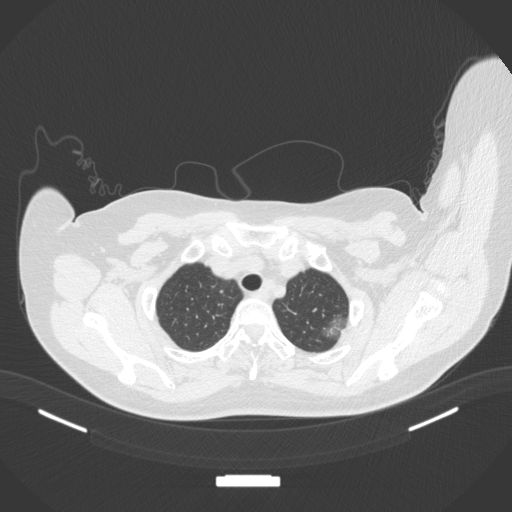
Chest CT, one axial slice; slice 321 of 386 in the series (ordered by position); reconstruction kernel B31f; 120 kVp; lung window (W 1500 / L -600 HU); 1 mm slice thickness; 512 × 512 image matrix. Patient: female, 58 years. Case-level facts recorded for this patient, not image findings: clinical TNM (as recorded): T1c N0 M0.
Outlined on this slice (rectangle marked by the reading radiologist):
- lung tumour (recorded histology: adenocarcinoma): bounding box [x1, y1, x2, y2] px = [317, 314, 351, 342]